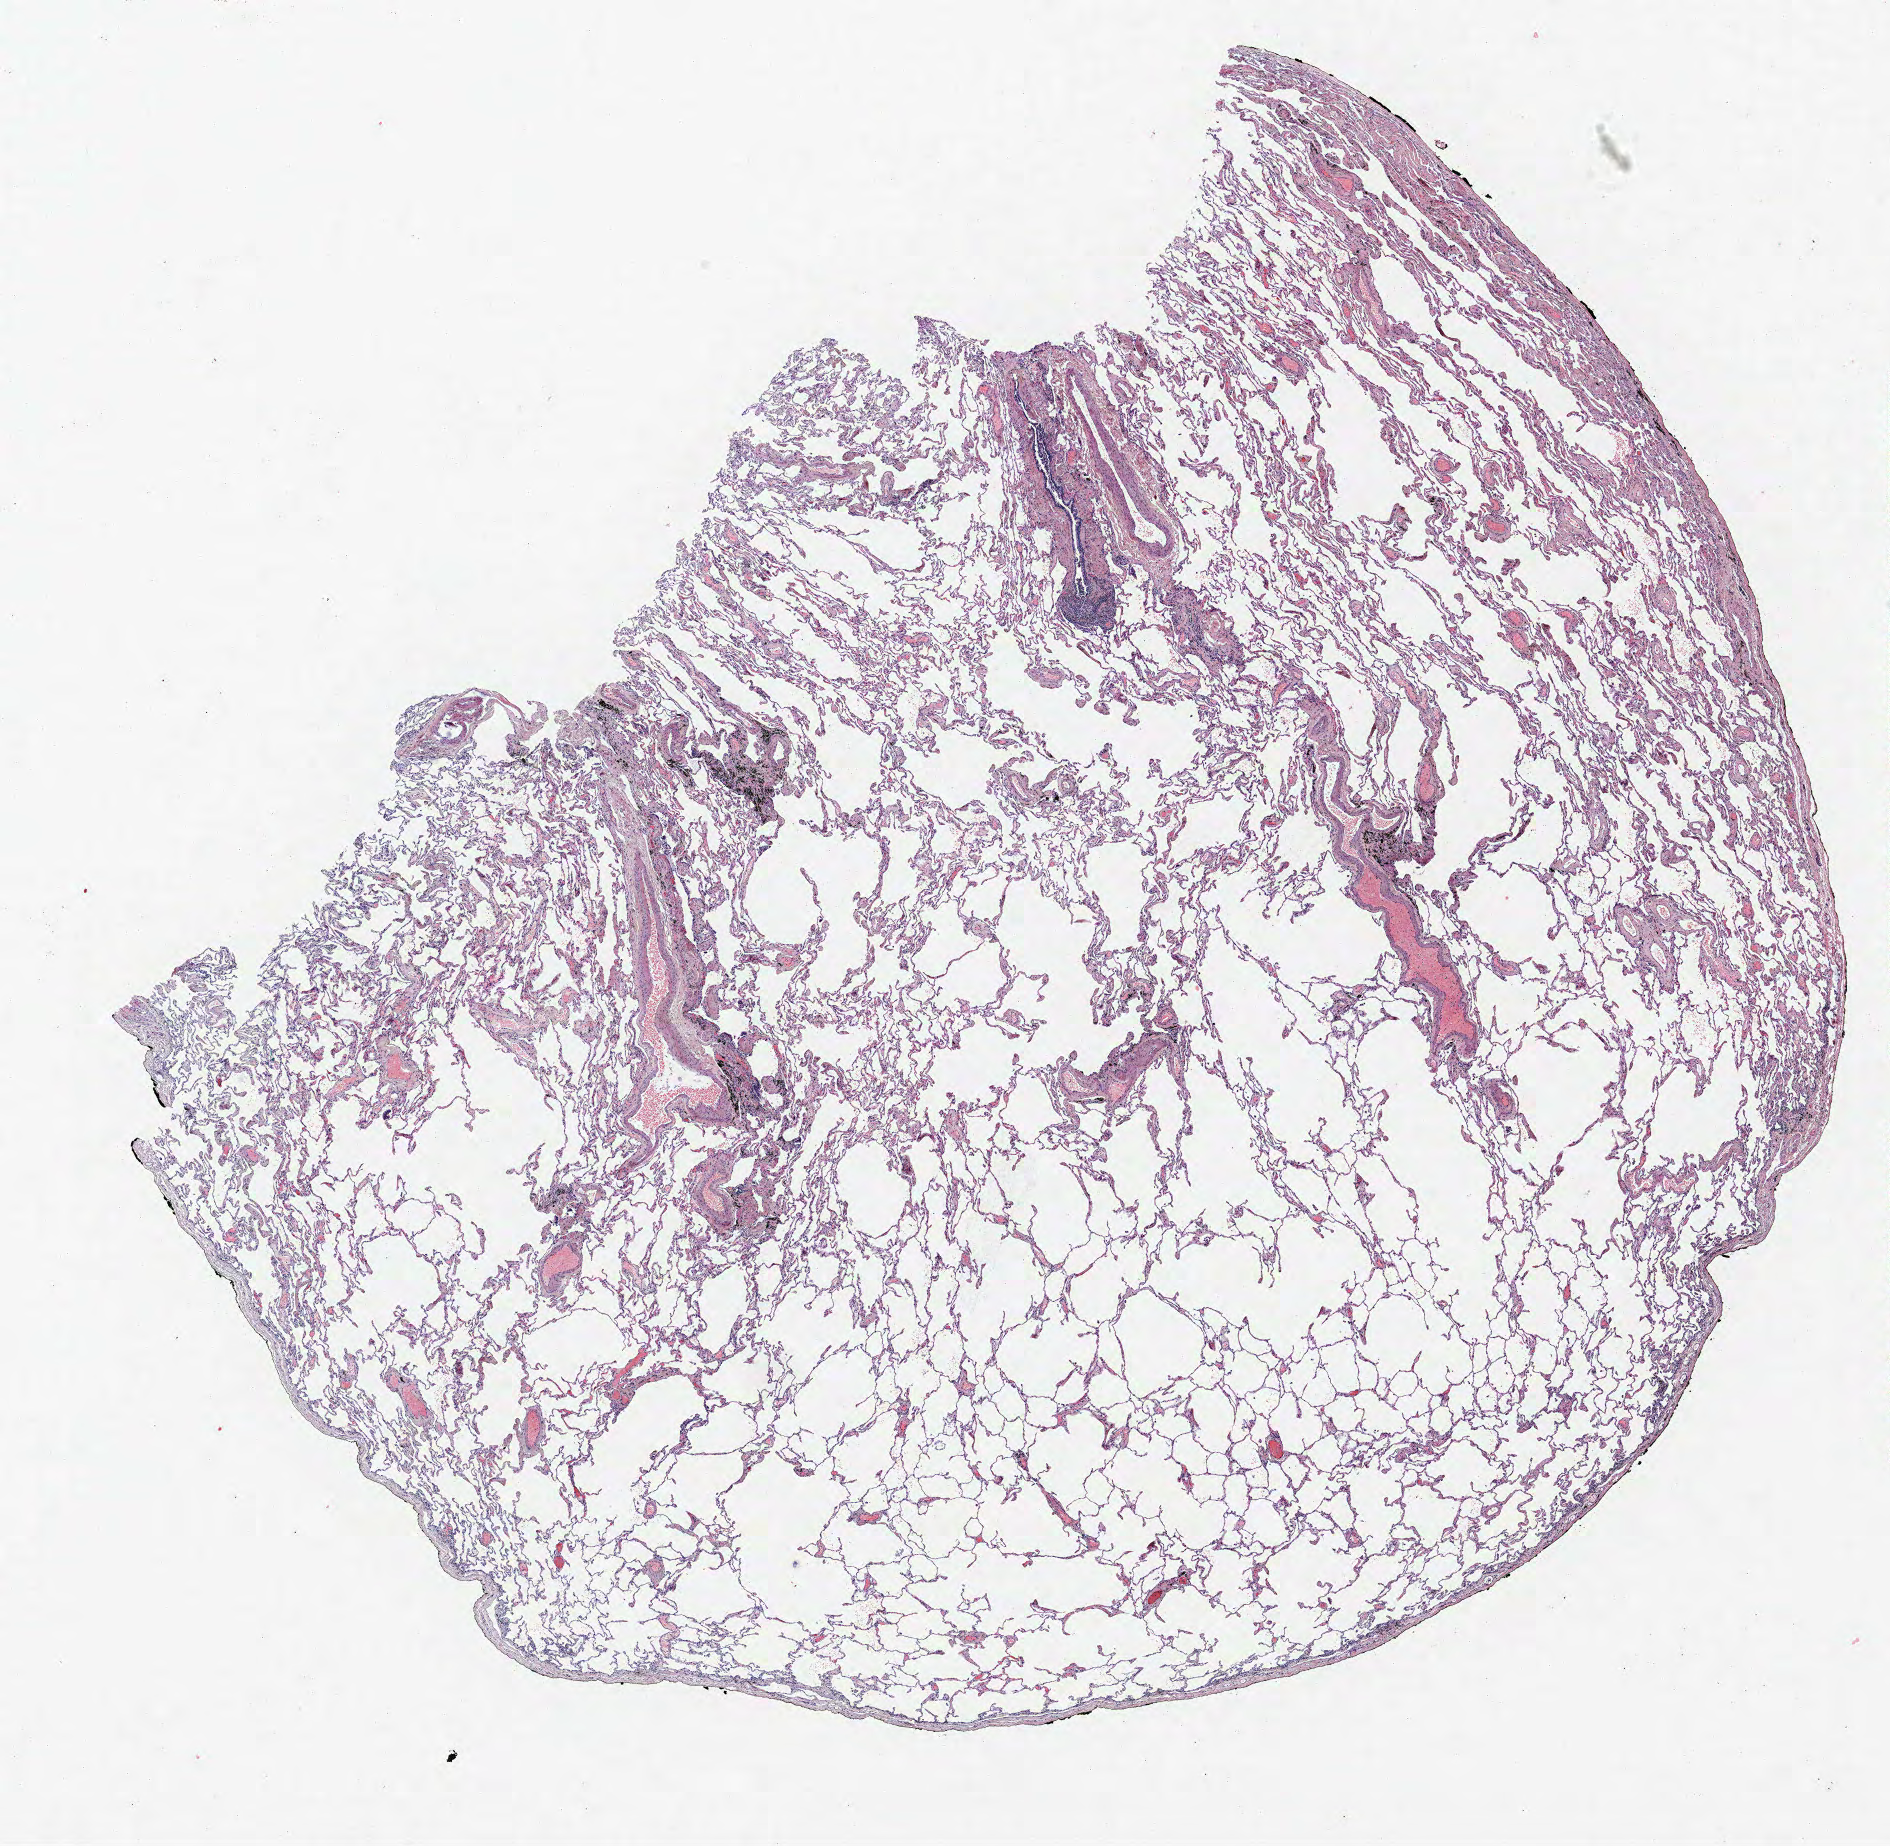
Hematoxylin and eosin (H&E) stained whole-slide image — low-resolution overview of the scanned area, about 15.1 x 14.8 mm. FFPE section. Lung tissue. Male patient, aged 69 at enrolment. Former smoker at enrolment. Grade: poorly differentiated (G3).
* participant's lung-cancer diagnosis: Squamous cell carcinoma, NOS (ICD-O-3 8070/3)
* primary tumour location (clinical record): left upper lobe
* stage (AJCC 6th edition): IV
* ICD-O-3 topography: upper lobe of lung (C34.1)
* tumour size (pathology): 18 mm